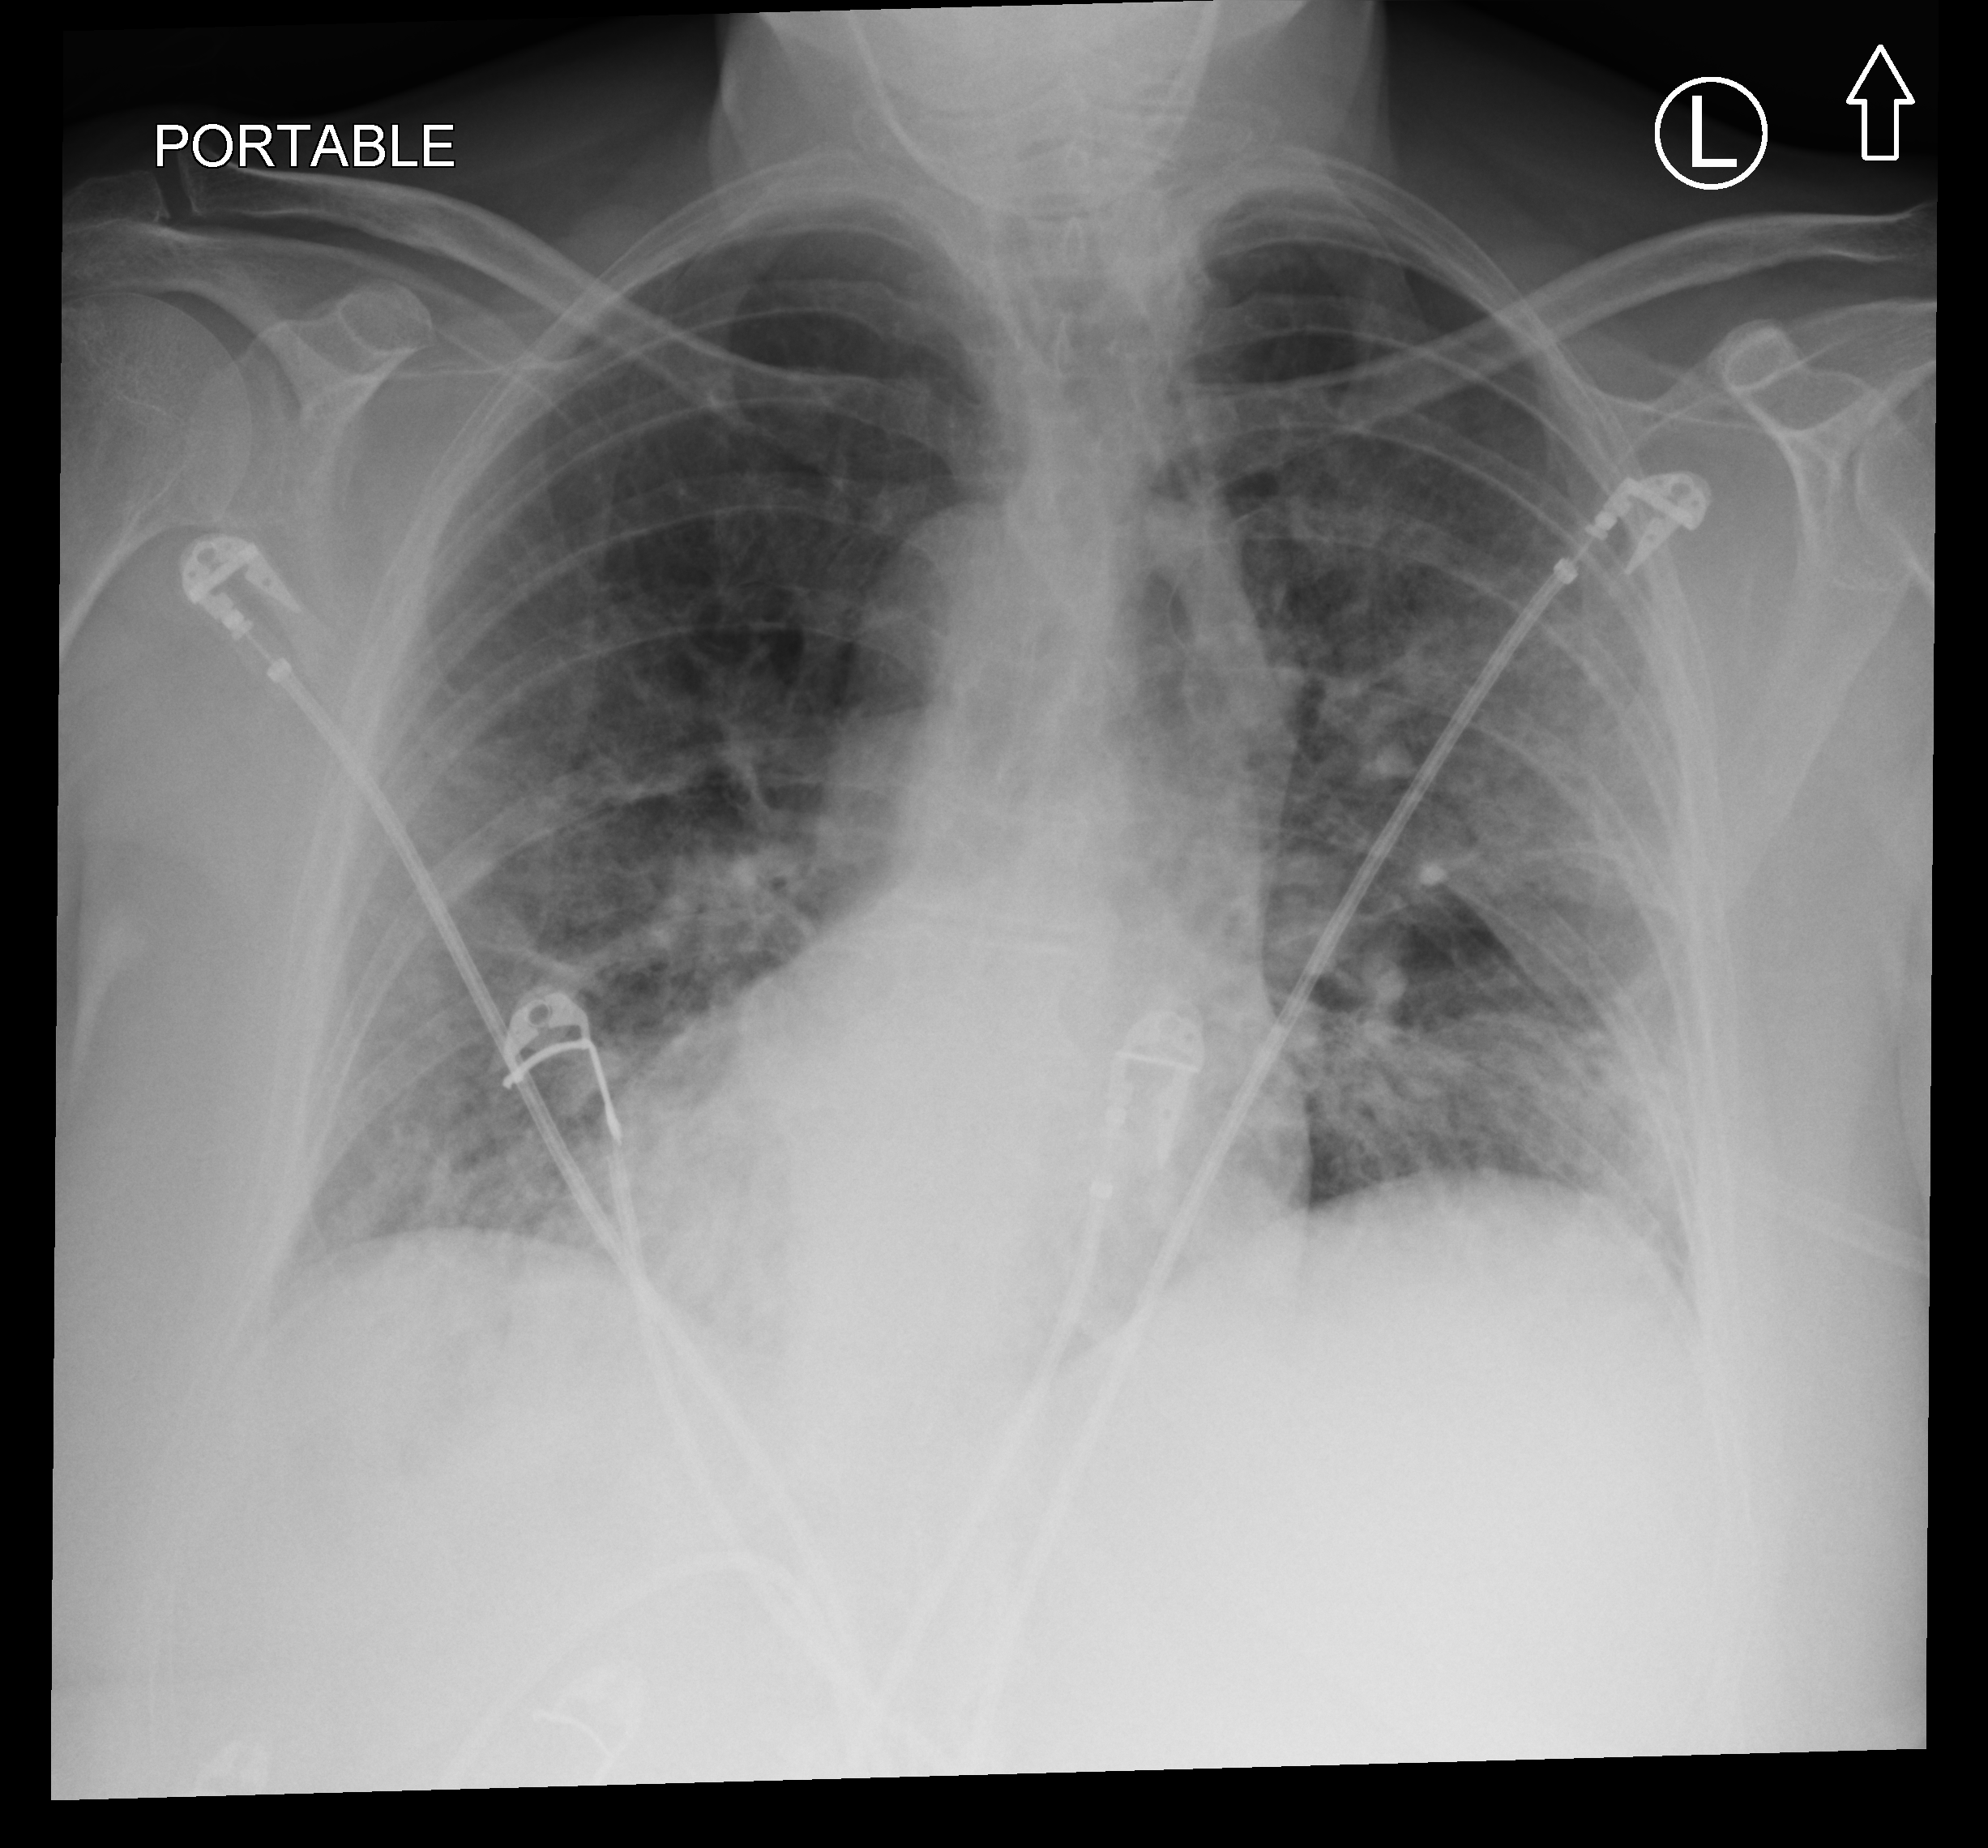
Bedside chest radiograph (computed radiography), anteroposterior (AP) projection. Patient hospitalised with COVID-19; female, aged 60–74 years.
Admission-level facts for this patient (not findings on this image; timing relative to this image not recorded):
- mechanically ventilated during this hospital stay: no
- admitted to intensive care during this hospital stay: no